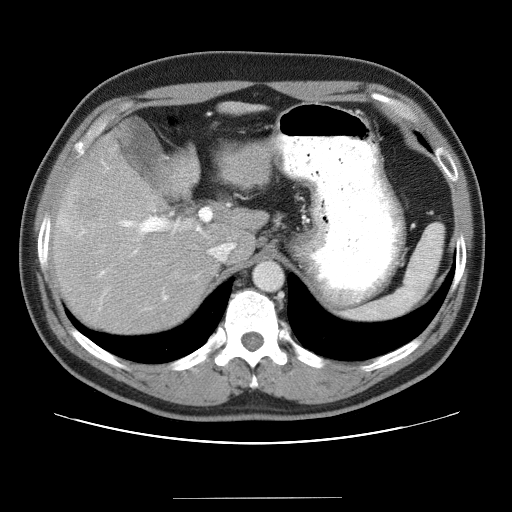
Contrast-enhanced abdominal CT (liver protocol), one axial slice. Position 25 of 40 along the scan axis. Reconstruction kernel STANDARD. 120 kVp. Soft-tissue window (W 400 / L 40 HU). 5 mm slice thickness. 512 × 512 image matrix, field of view 380 × 380 mm. Case-level facts recorded for this patient, not image findings: diagnosis: hepatocellular carcinoma (patient treated with transarterial chemoembolisation; whether this scan precedes or follows treatment is not stated here); TNM stage (as recorded): Stage-IVA; Child-Pugh class: B.
Structures marked on this image (semi-automatic segmentation, software-assisted and operator-edited):
- abdominal aorta: bounding box [x1, y1, x2, y2] px = [254, 262, 281, 290]
- liver parenchyma outside the tumour (the mass and vessels are separate outlines, so this box may not span the whole liver): [52, 102, 268, 332]
- mass: [55, 174, 108, 238]
- liver vessels: [99, 204, 229, 310]